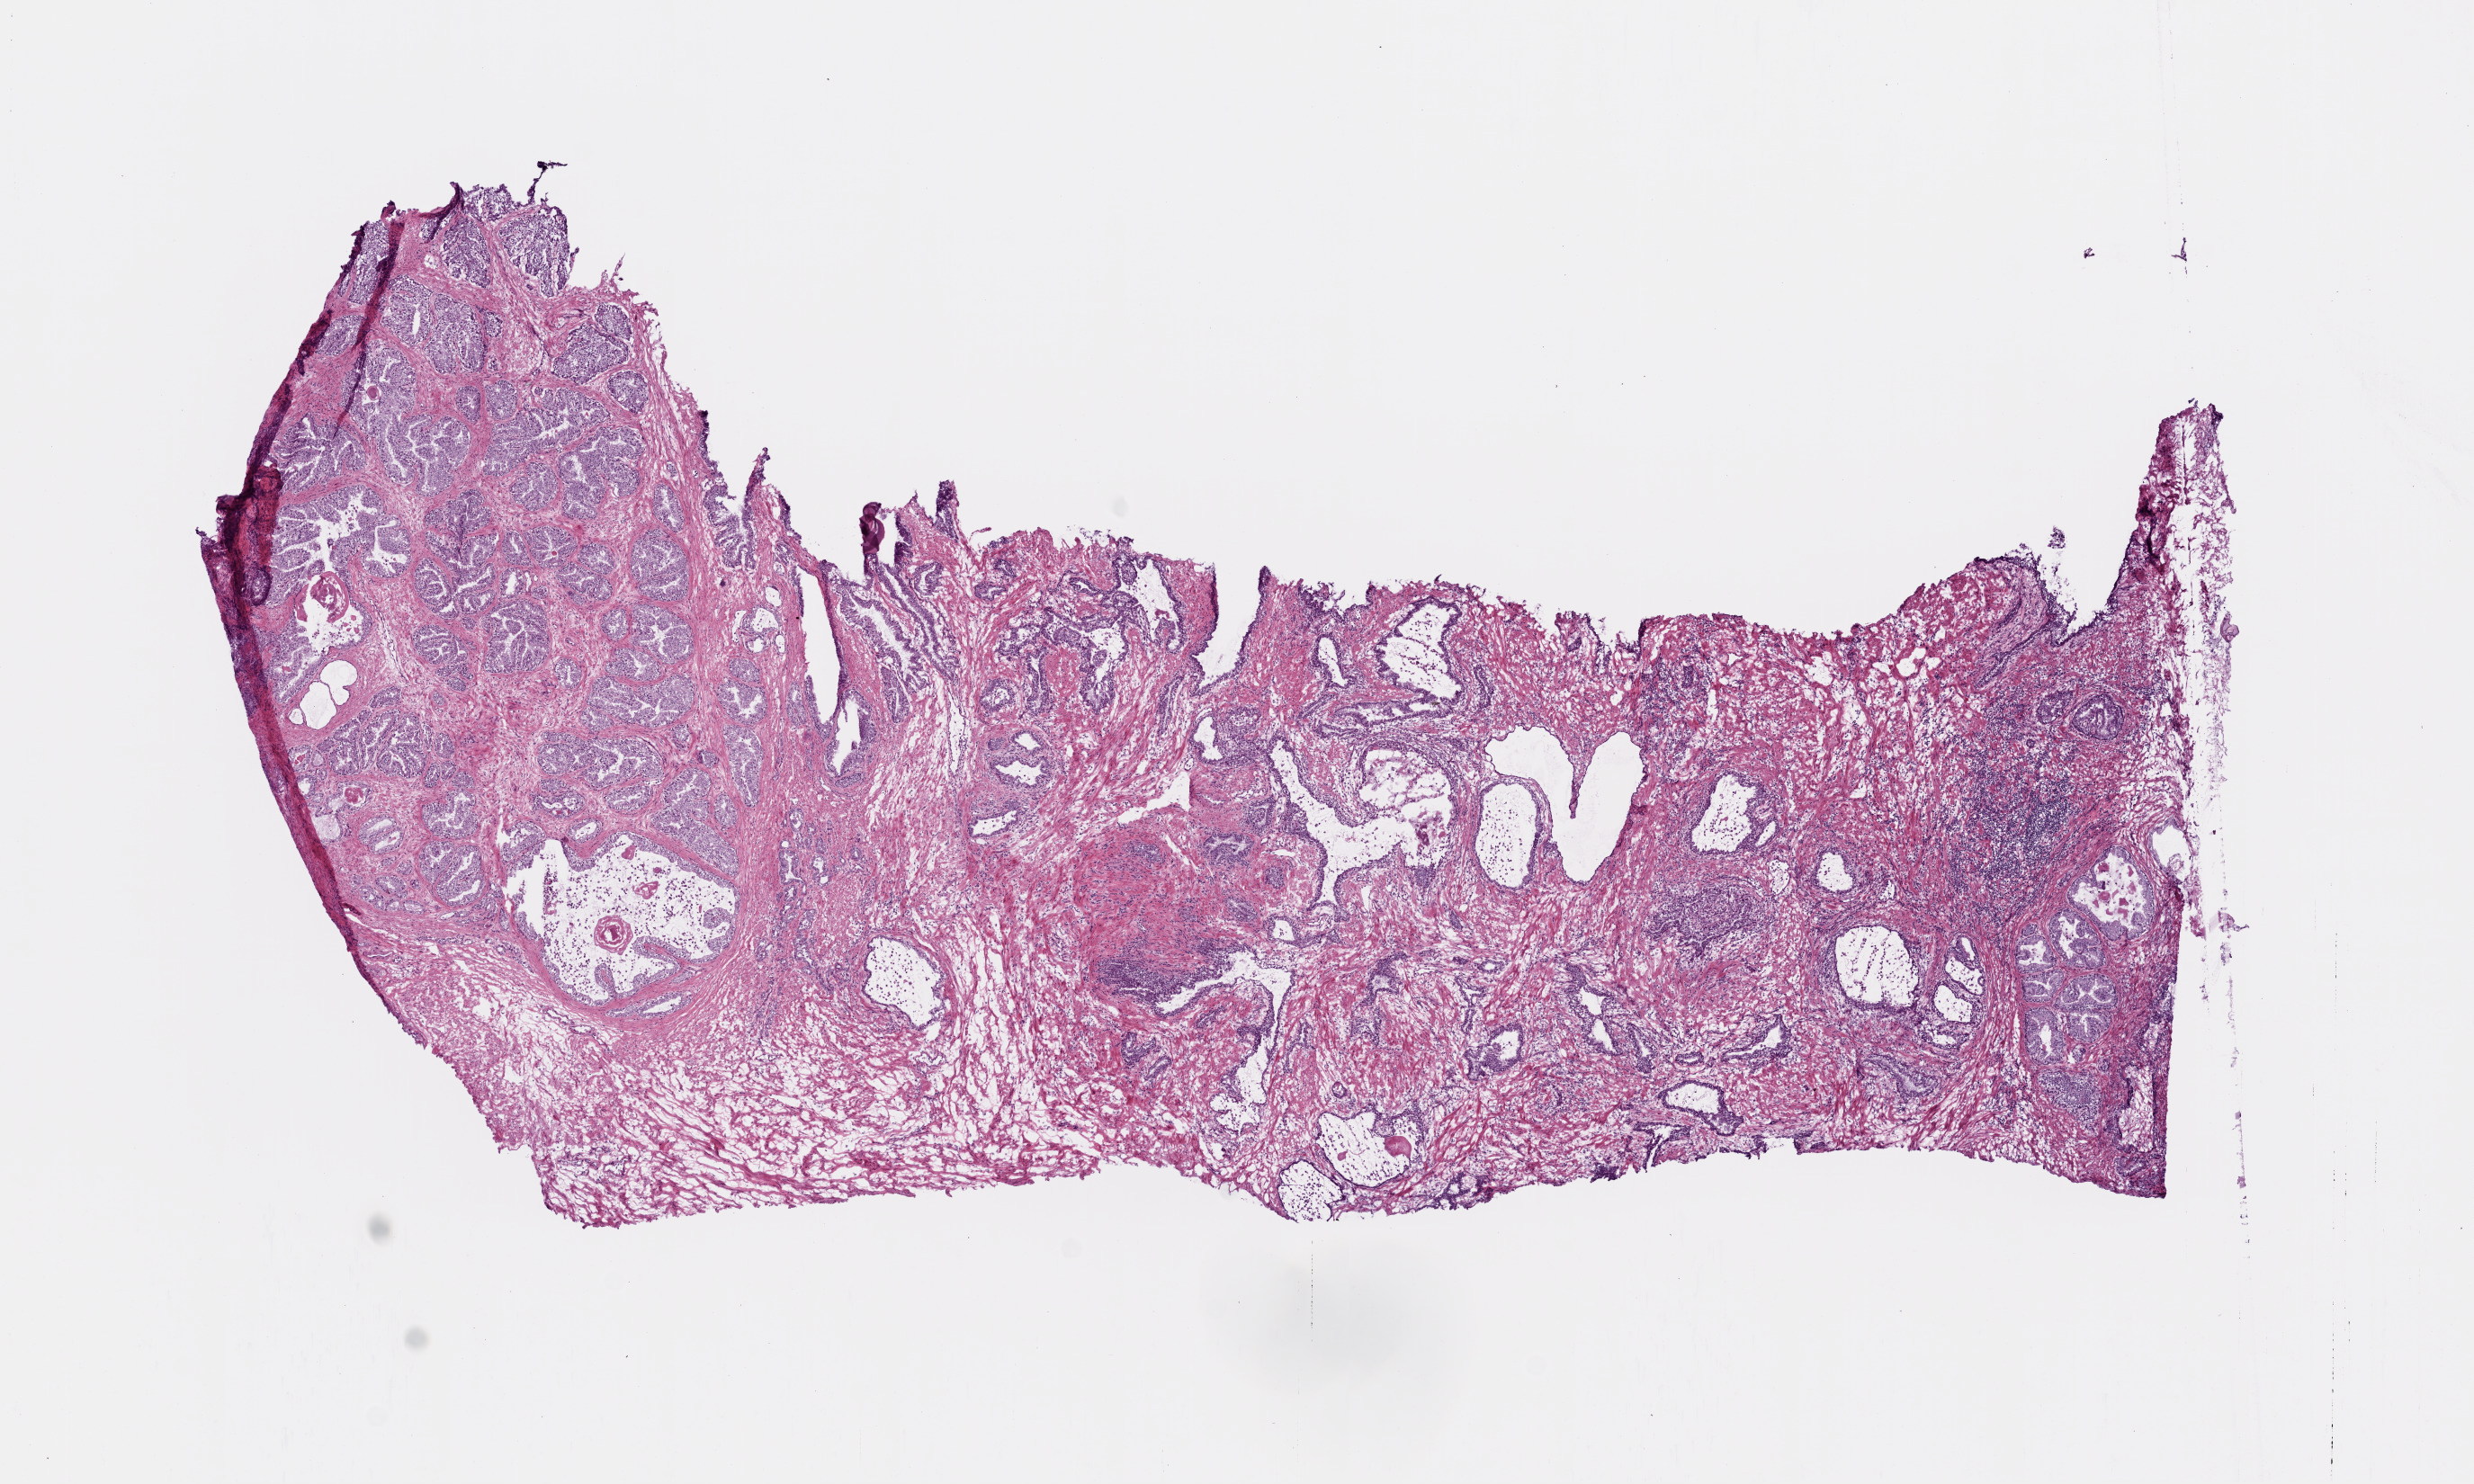
Whole-slide histology image, H&E-stained, low-resolution overview of the scanned area, about 11.0 x 6.6 mm (slide scanned at 20x). Frozen section from the top of the tissue portion. Prostate, solid tissue normal (non-tumour tissue) sample. Male patient; age at initial diagnosis 66 years.
This section: solid tissue normal (non-tumour) sample from the same patient. Patient diagnosis: Acinar cell carcinoma (prostate gland).